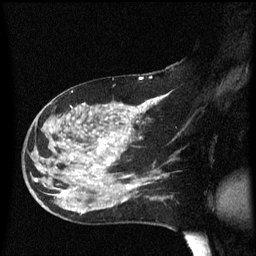
Breast MRI (dynamic contrast-enhanced), one sagittal slice; position 32 of 60 along the scan axis; dynamic contrast-enhanced series, image 2 of 3 at this slice position (ordered by acquisition); 1.5 T; TE 4.2 ms, TR 8.4 ms; 256 × 256 image matrix. Female patient, age 47 years.
Outlined on this slice (semi-automatically segmented with operator editing):
- analysis volume of interest (the breast-tissue region the enhancement analysis was run in; not a lesion): bounding box [x1, y1, x2, y2] px = [24, 97, 149, 206]
- tumour enhancement mask (voxels above the 70 % enhancement threshold inside the analysis volume of interest): [34, 101, 149, 201]